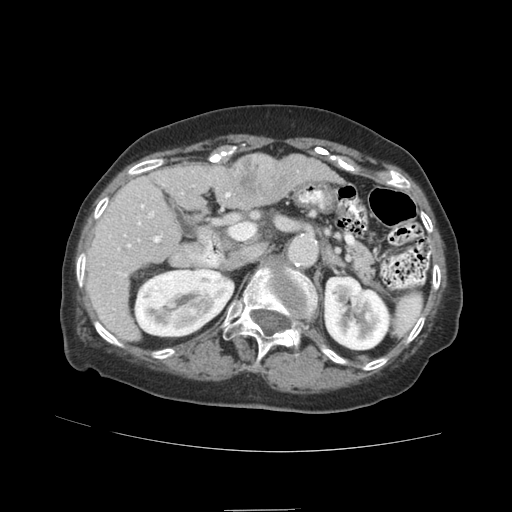
Contrast-enhanced abdominal CT (liver protocol), one axial slice; slice 48 of 89 in the series (ordered by position); reconstruction kernel STANDARD; 140 kVp; soft-tissue window (W 400 / L 40 HU); 2.5 mm slice thickness; 512 × 512 image matrix, field of view 360 × 360 mm. Case-level facts recorded for this patient, not image findings: diagnosis: hepatocellular carcinoma (patient treated with transarterial chemoembolisation; whether this scan precedes or follows treatment is not stated here); TNM stage (as recorded): Stage-II.
Outlined on this slice (semi-automatic segmentation, software-assisted and operator-edited):
- liver parenchyma outside the tumour (the mass and vessels are separate outlines, so this box may not span the whole liver): bounding box (x1, y1, x2, y2) in pixels: (86, 158, 338, 340)
- mass: (229, 154, 286, 206)
- liver vessels: (99, 171, 209, 318)